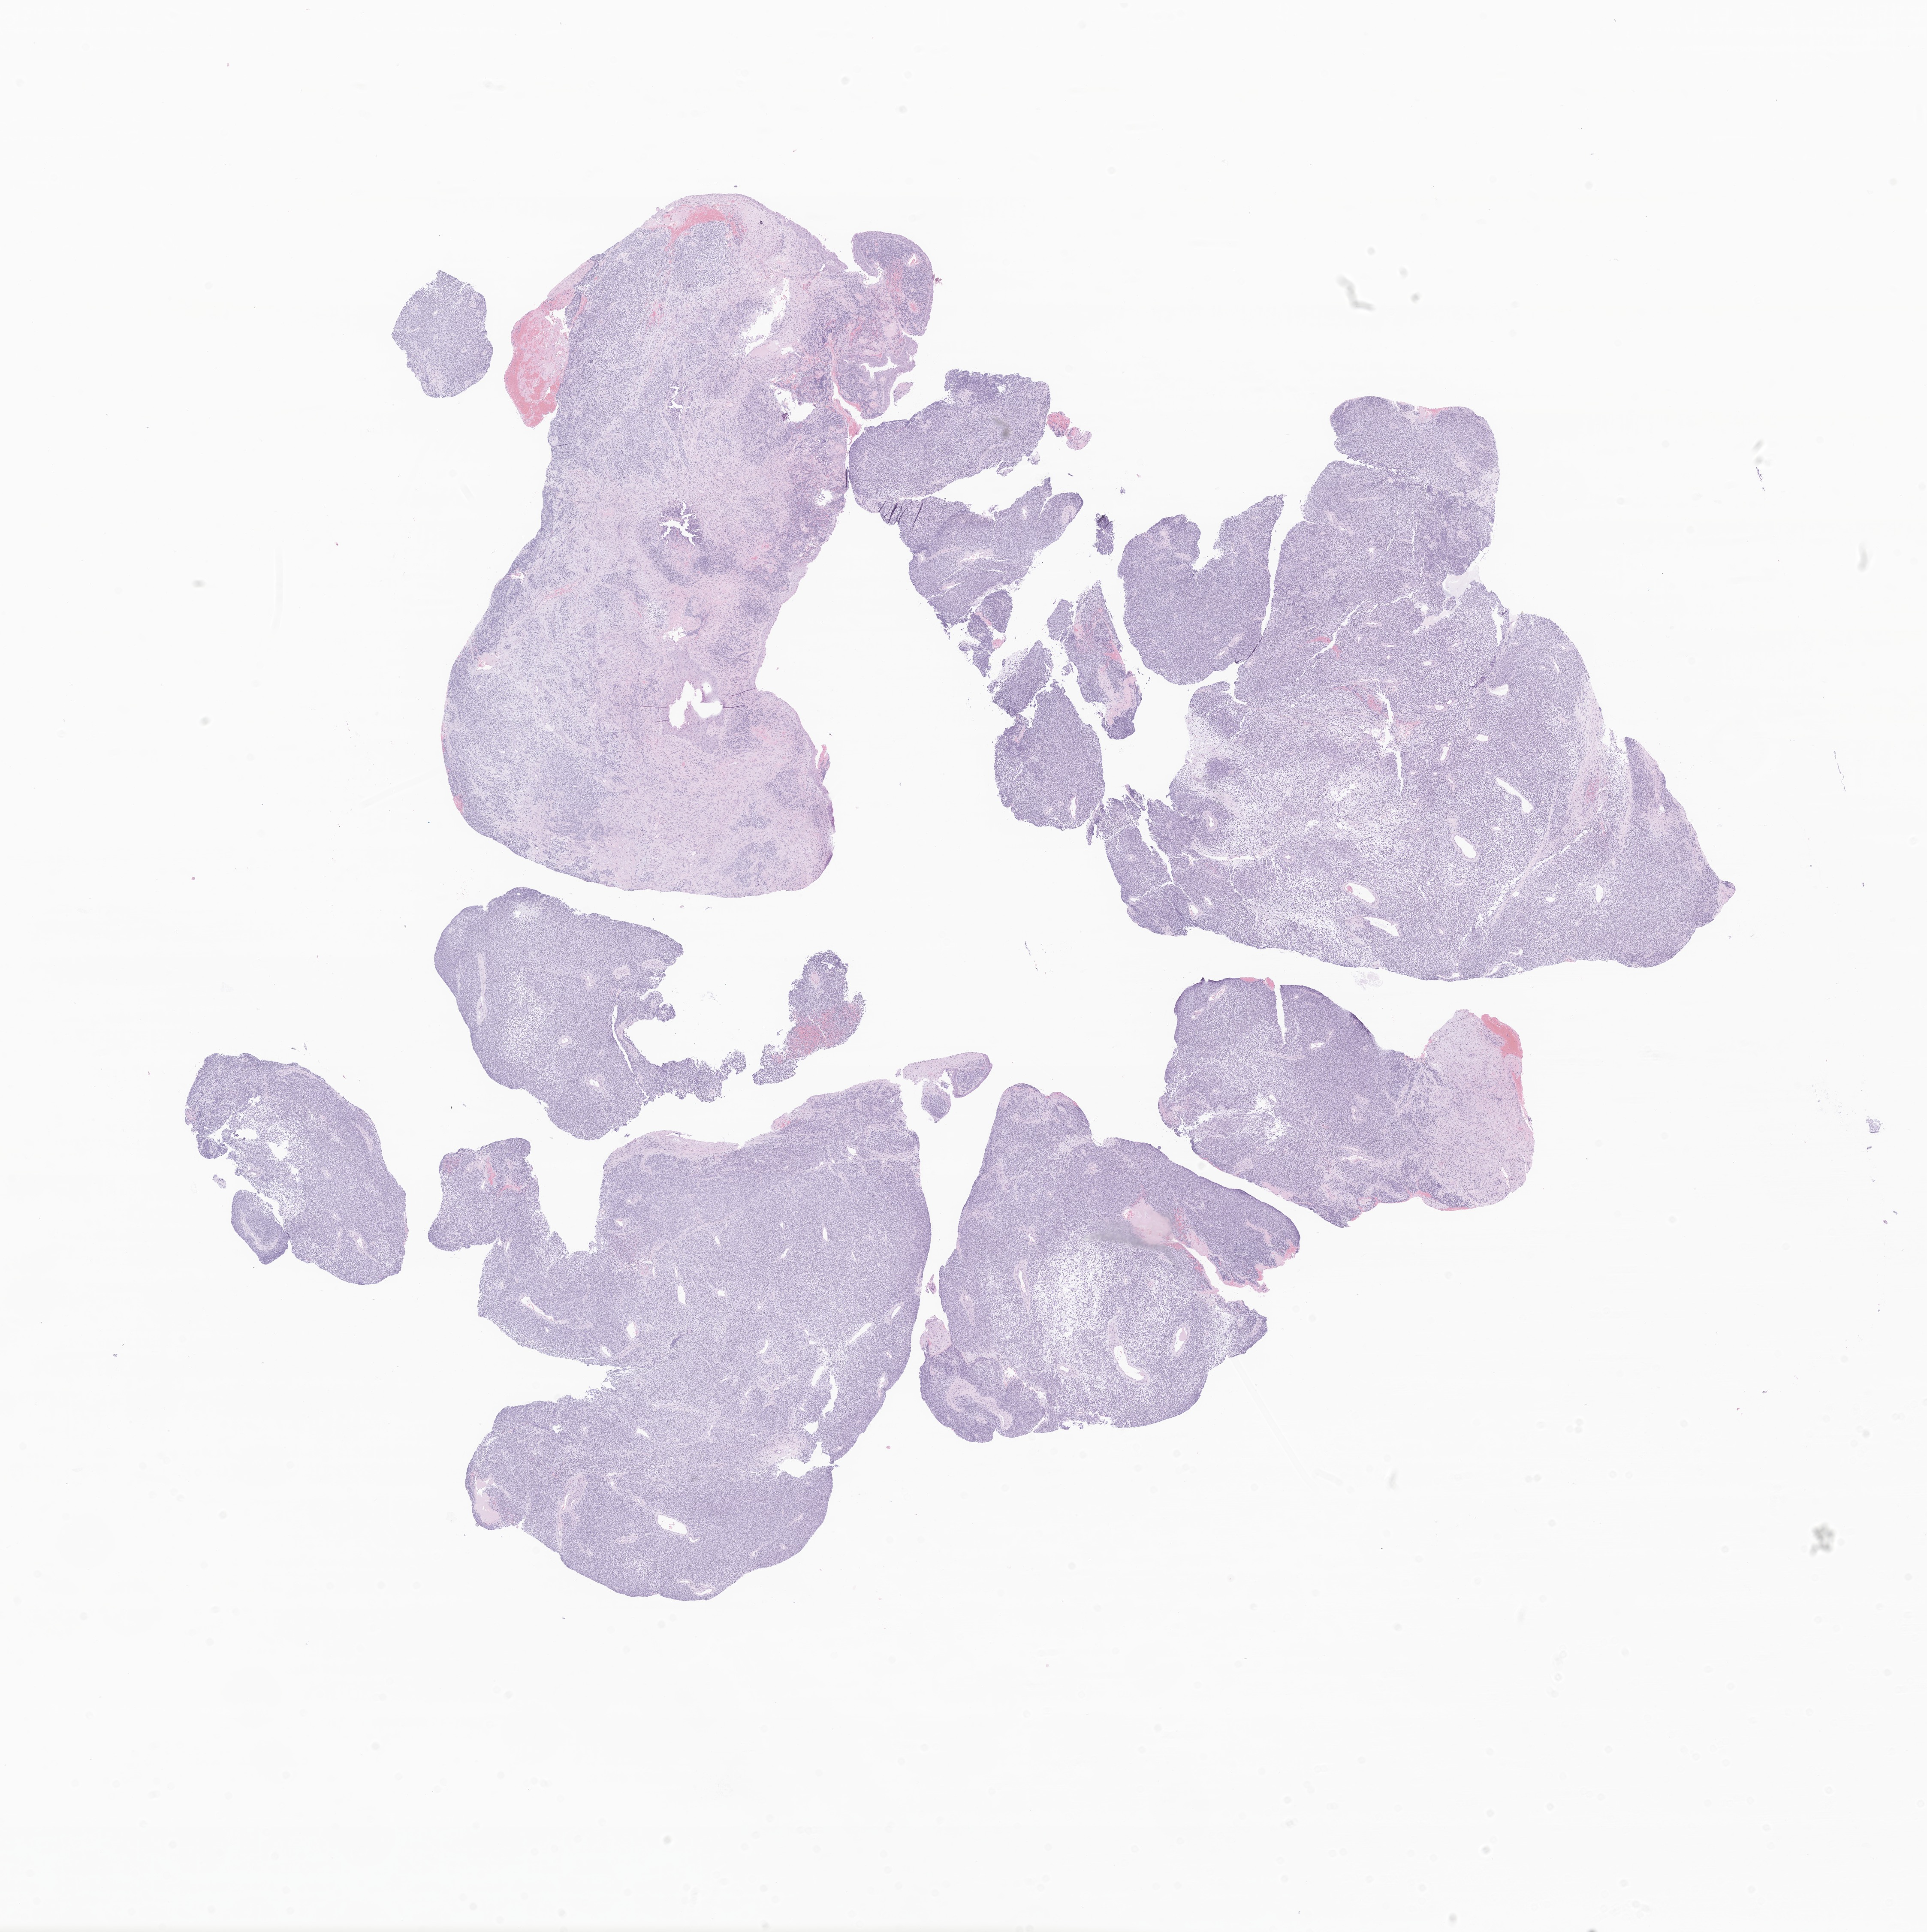
Haematoxylin and eosin whole-slide image of tumor tissue from the cranial and/or facial bone, a low-resolution overview of the entire scanned area, about 18.9 x 19.0 mm. Formalin-fixed, paraffin-embedded (FFPE) tissue. Male patient, age 56 months (4 years 8 months).
• diagnosis: Tumor cells, malignant
• tissue or organ of origin (case record): bones of skull and face and associated joints